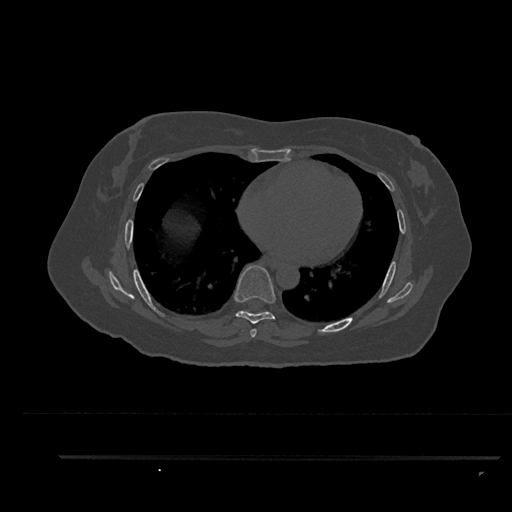
CT including the spine, one axial slice. Slice 505 of 797 in the series (ordered by position). 120 kVp. Bone window (W 1800 / L 400 HU). 0.5 mm slice thickness. 512 × 512 image matrix, field of view 408 × 408 mm. Patient: female, 44 years. Case-level facts recorded for this patient, not image findings: primary cancer: renal; vertebrae with lytic lesions (as recorded): L1.
Annotated regions visible in this slice (semi-automatic segmentation, software-assisted and operator-edited):
- T6 vertebra: box from (x=250, y=328) to (x=257, y=338) px
- T7 vertebra: (x=233, y=265)–(x=276, y=324)